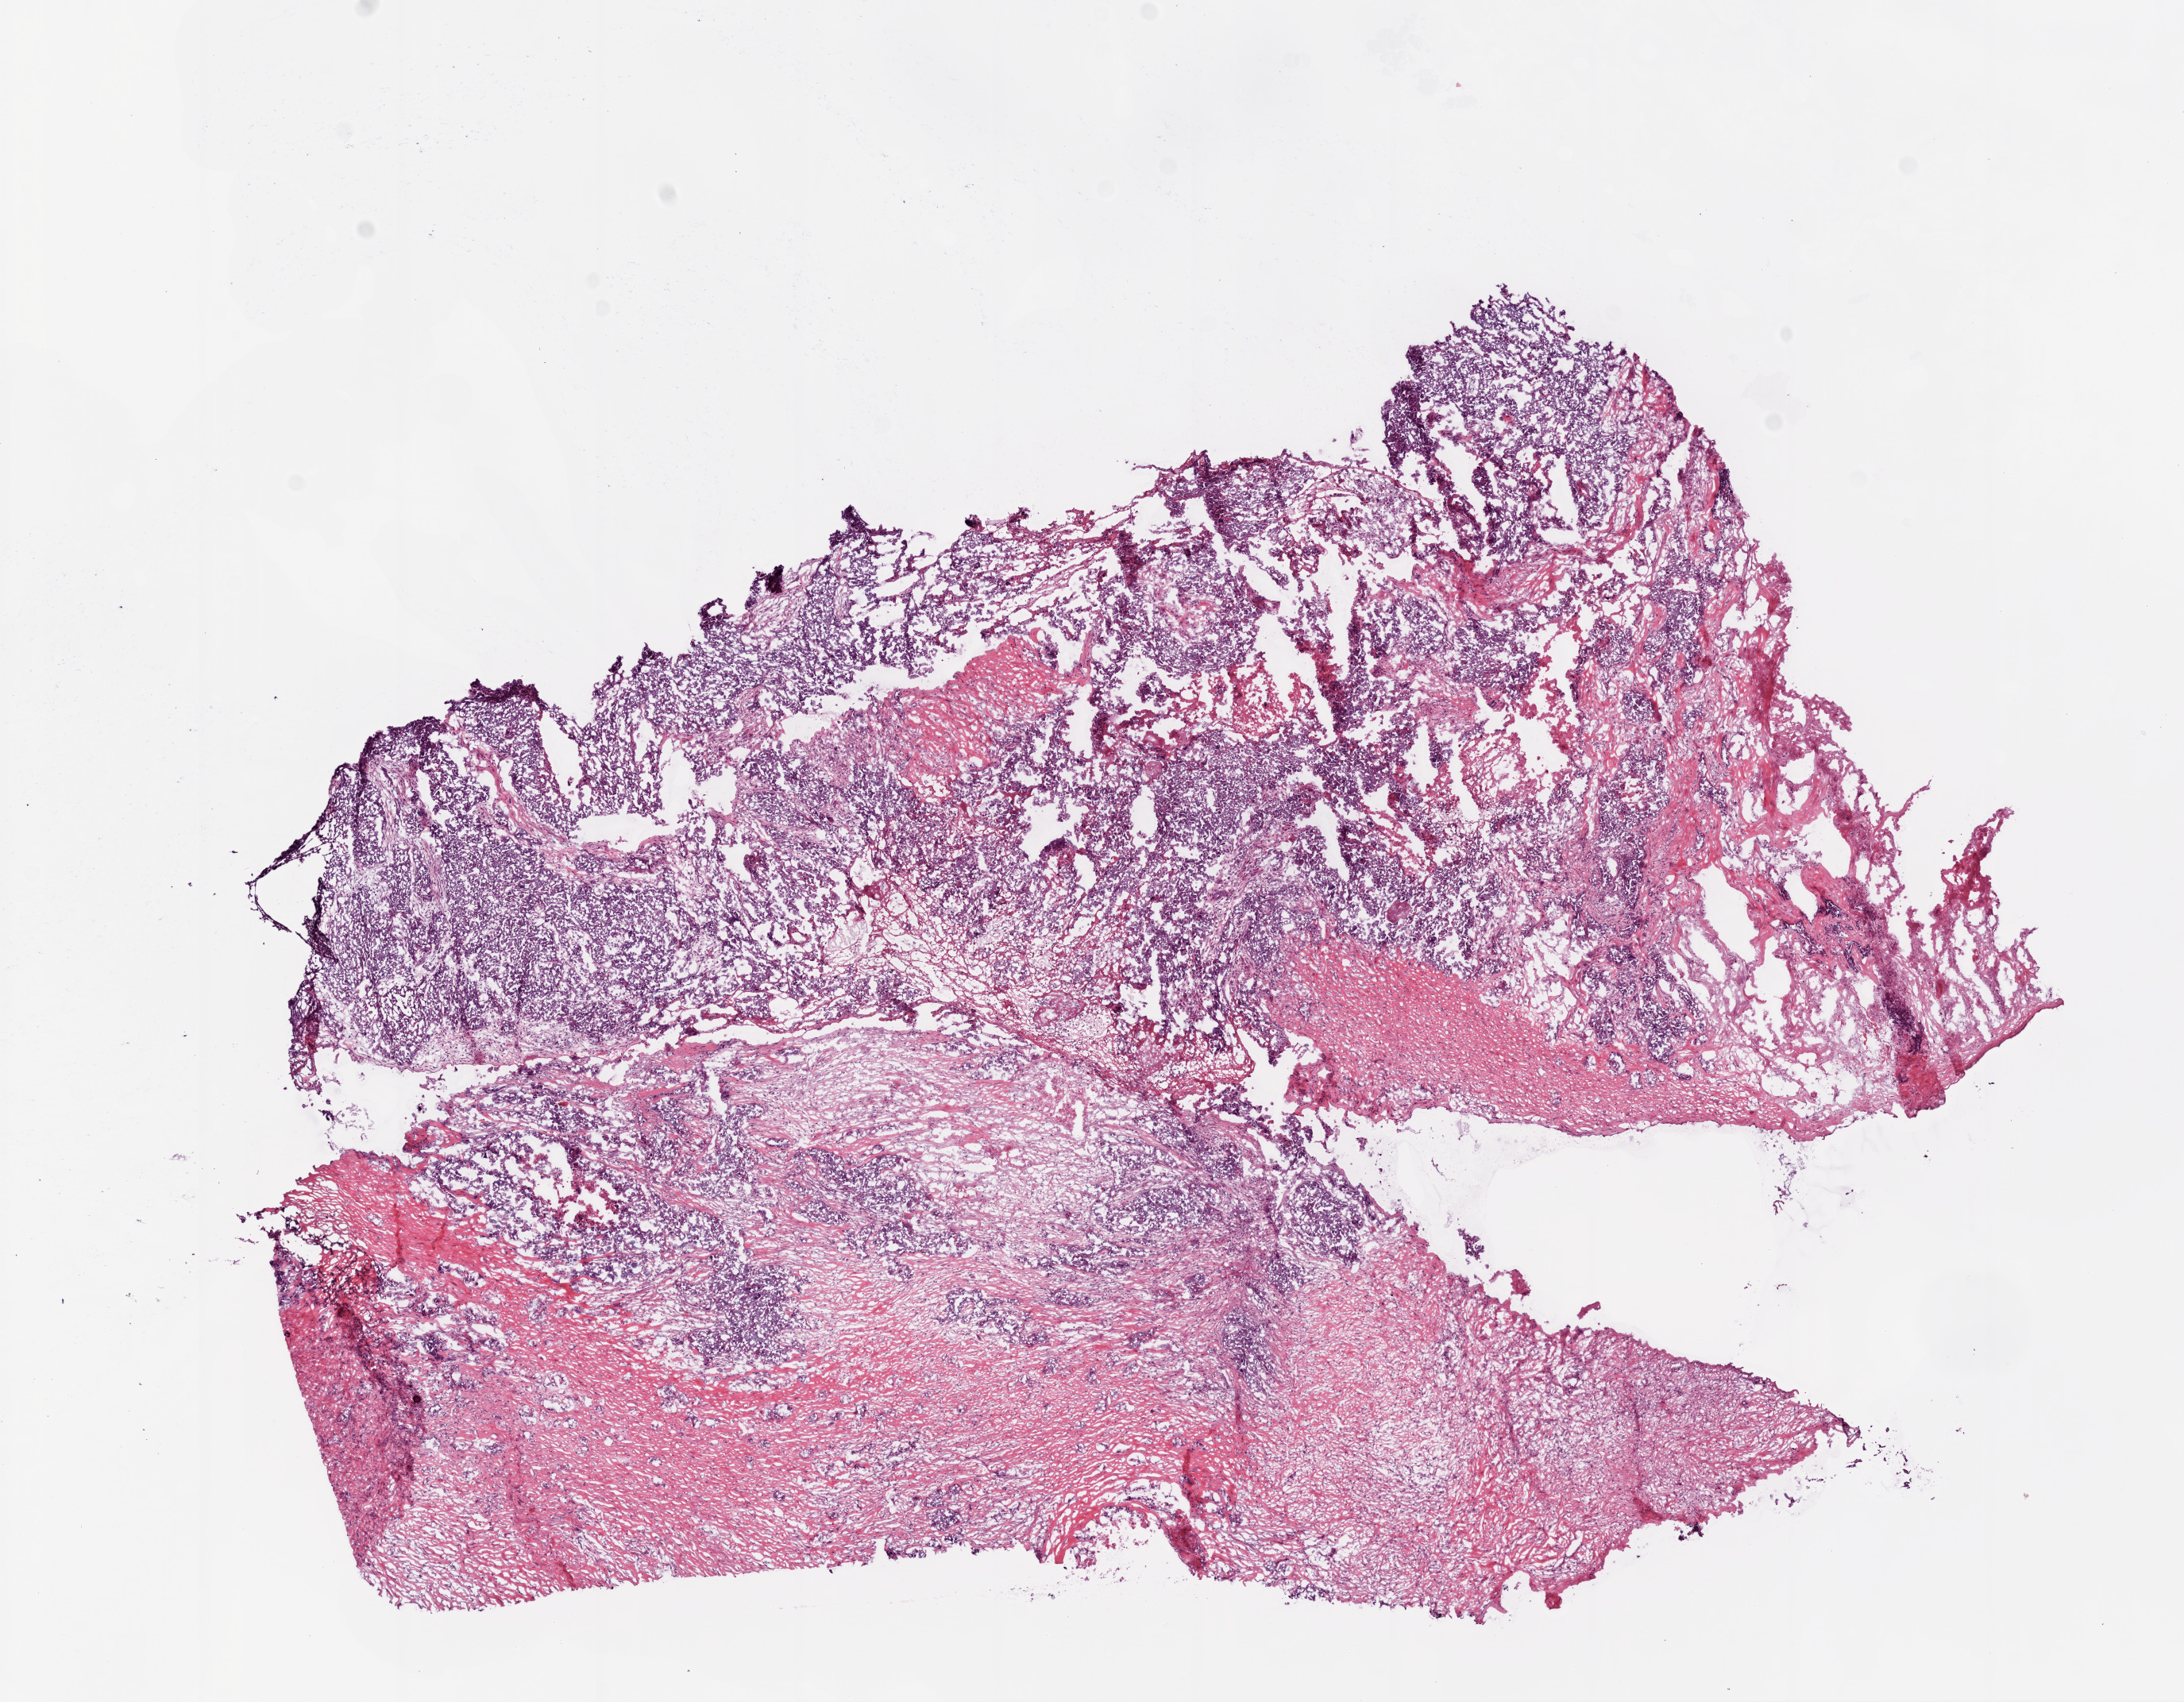
Digitized Hematoxylin and eosin (H&E) stained tissue section (whole slide) — low-resolution overview of the scanned area, about 11.0 x 8.6 mm (slide scanned at 20x), frozen section from the bottom of the tissue portion, primary tumour sample from the ovary. Patient: female, age at initial diagnosis 55 years. Histologic grade: G3 (poorly differentiated). Composition of this section per pathologist review: tumour cells 70%, tumour nuclei 88%, normal cells 27%, stromal cells 0%, necrosis 3%.
Laterality: bilateral. Diagnosis: Serous cystadenocarcinoma, NOS. FIGO stage: IIIC.